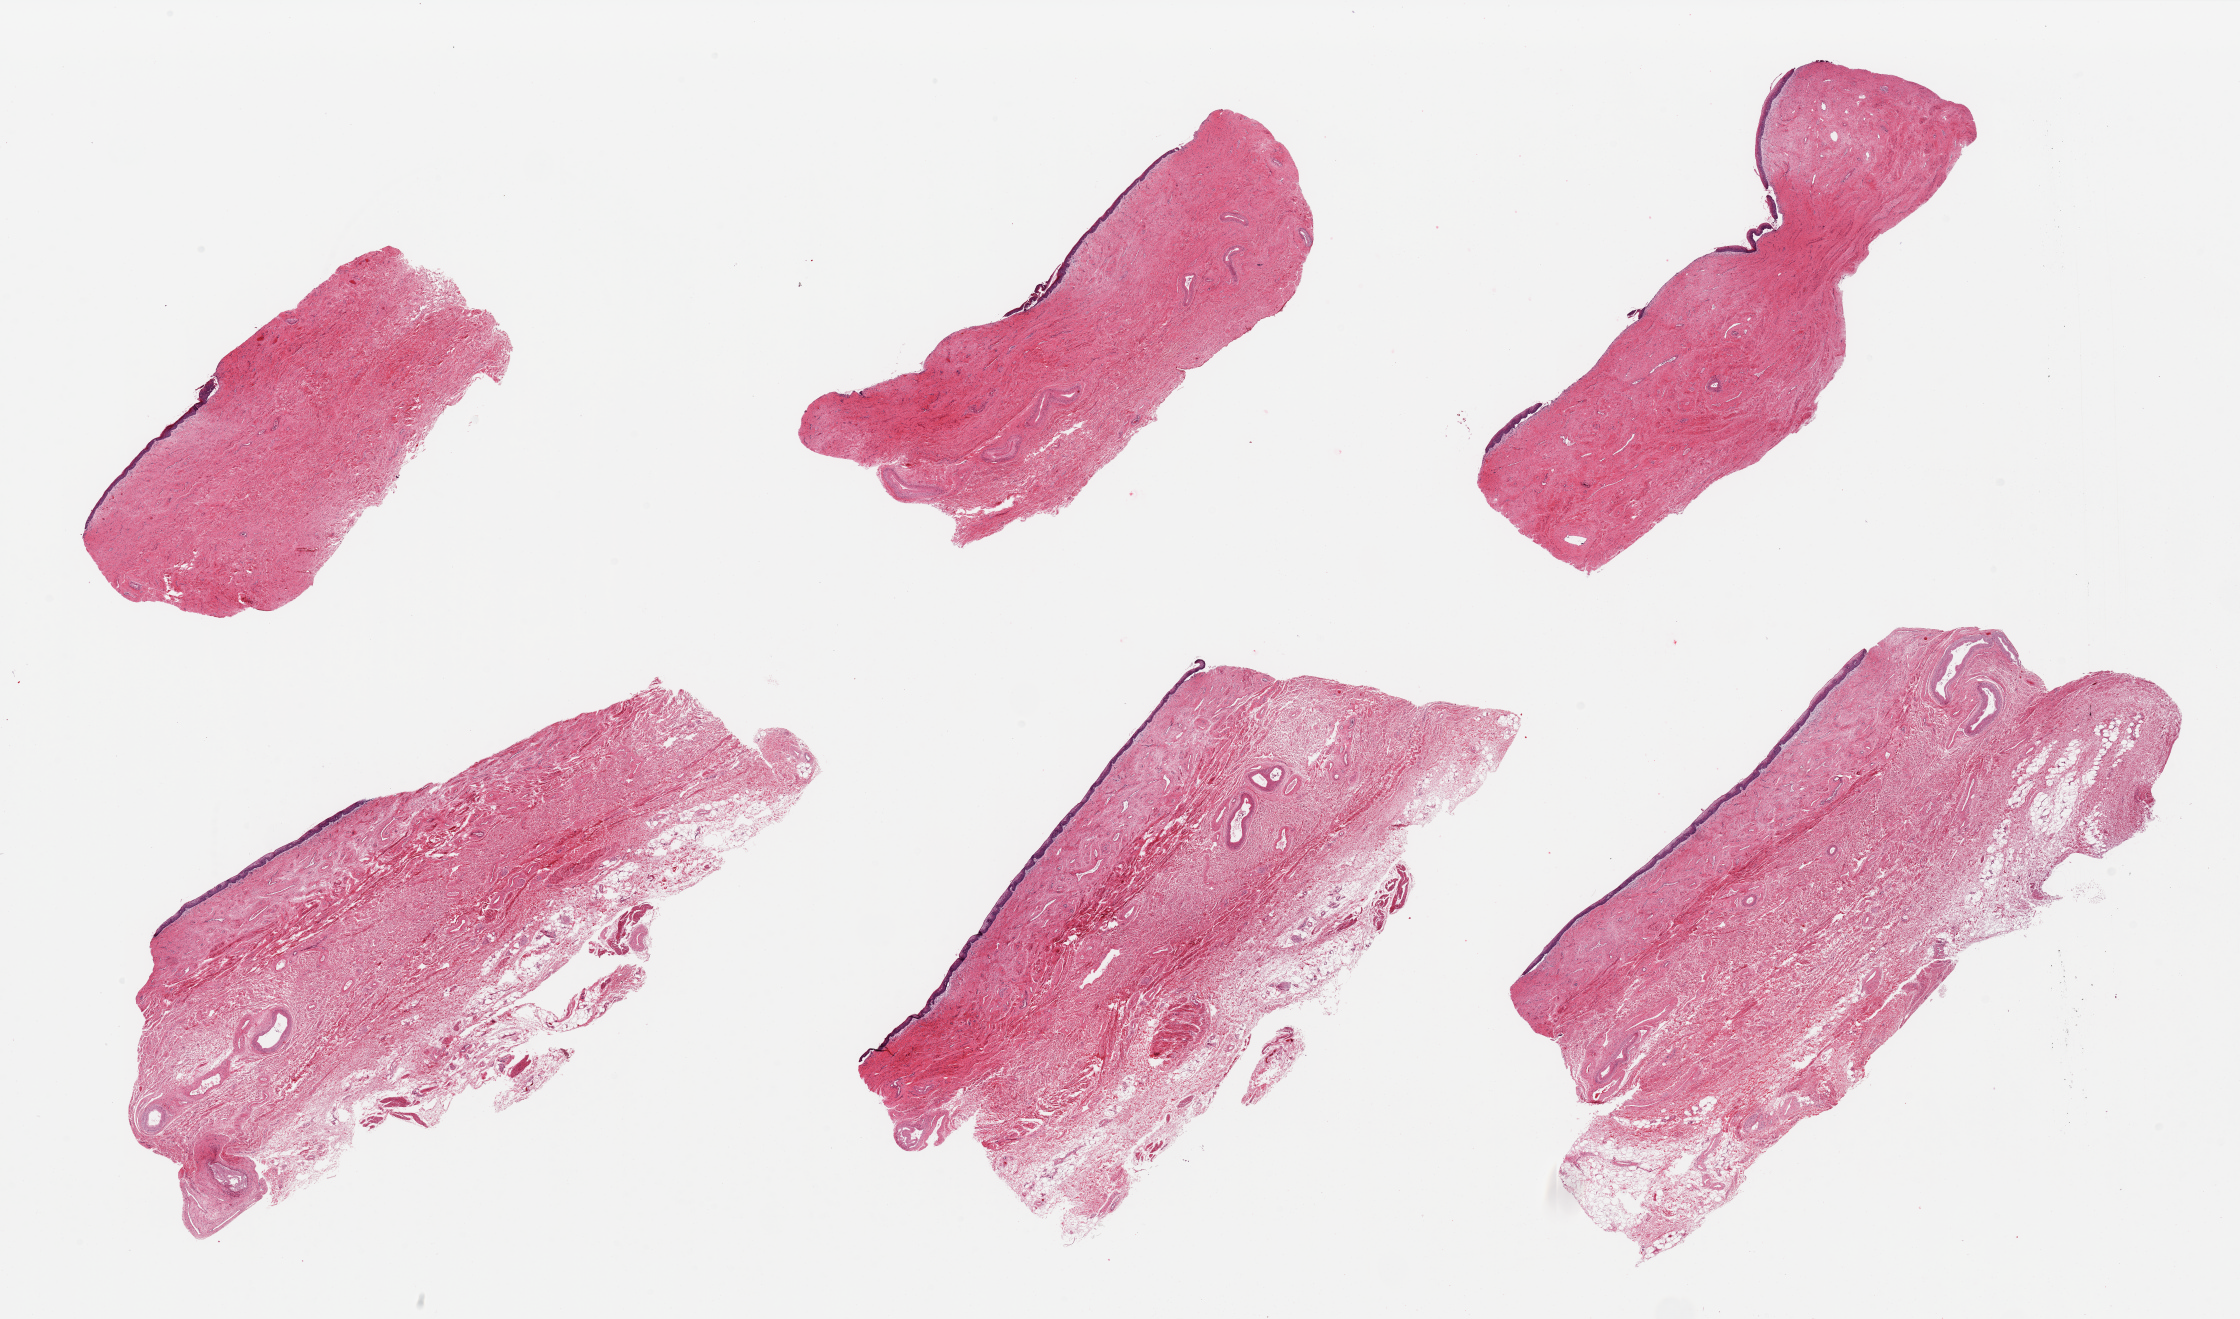
Digitized H&E-stained section, brightfield — low-resolution overview of the scanned area, about 35.4 x 20.9 mm, PAXgene-fixed, paraffin-embedded tissue, target tissue: vagina, tissue donor sample.
Review note (as recorded): 6 pieces; squamous mucosa is ~2.5% thickness.